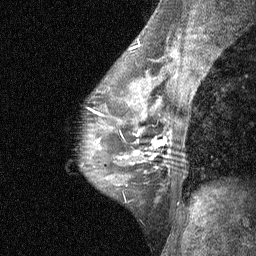
Breast MRI (dynamic contrast-enhanced), one sagittal slice; slice 40 of 64 in the series (ordered by position); dynamic contrast-enhanced study with each time point stored as its own series, time point 3 of 4 at this slice position (ordered by acquisition time); 1.5 T; TE 4.8 ms, TR 27 ms; 2 mm slice thickness; 256 × 256 image matrix, field of view 180 × 180 mm. Female patient, age 44 years. From the clinical record (not read from this slice): setting: breast cancer imaged before/during neoadjuvant chemotherapy; receptor status: HR-positive, HER2-negative.
Outlined on this slice (semi-automatically segmented with operator editing):
- analysis volume of interest (the breast-tissue region the enhancement analysis was run in; not a lesion): box from (x=115, y=117) to (x=185, y=188) px
- tumour enhancement mask (voxels above the 90 % enhancement threshold inside the analysis volume of interest): (x=134, y=139)–(x=170, y=159)